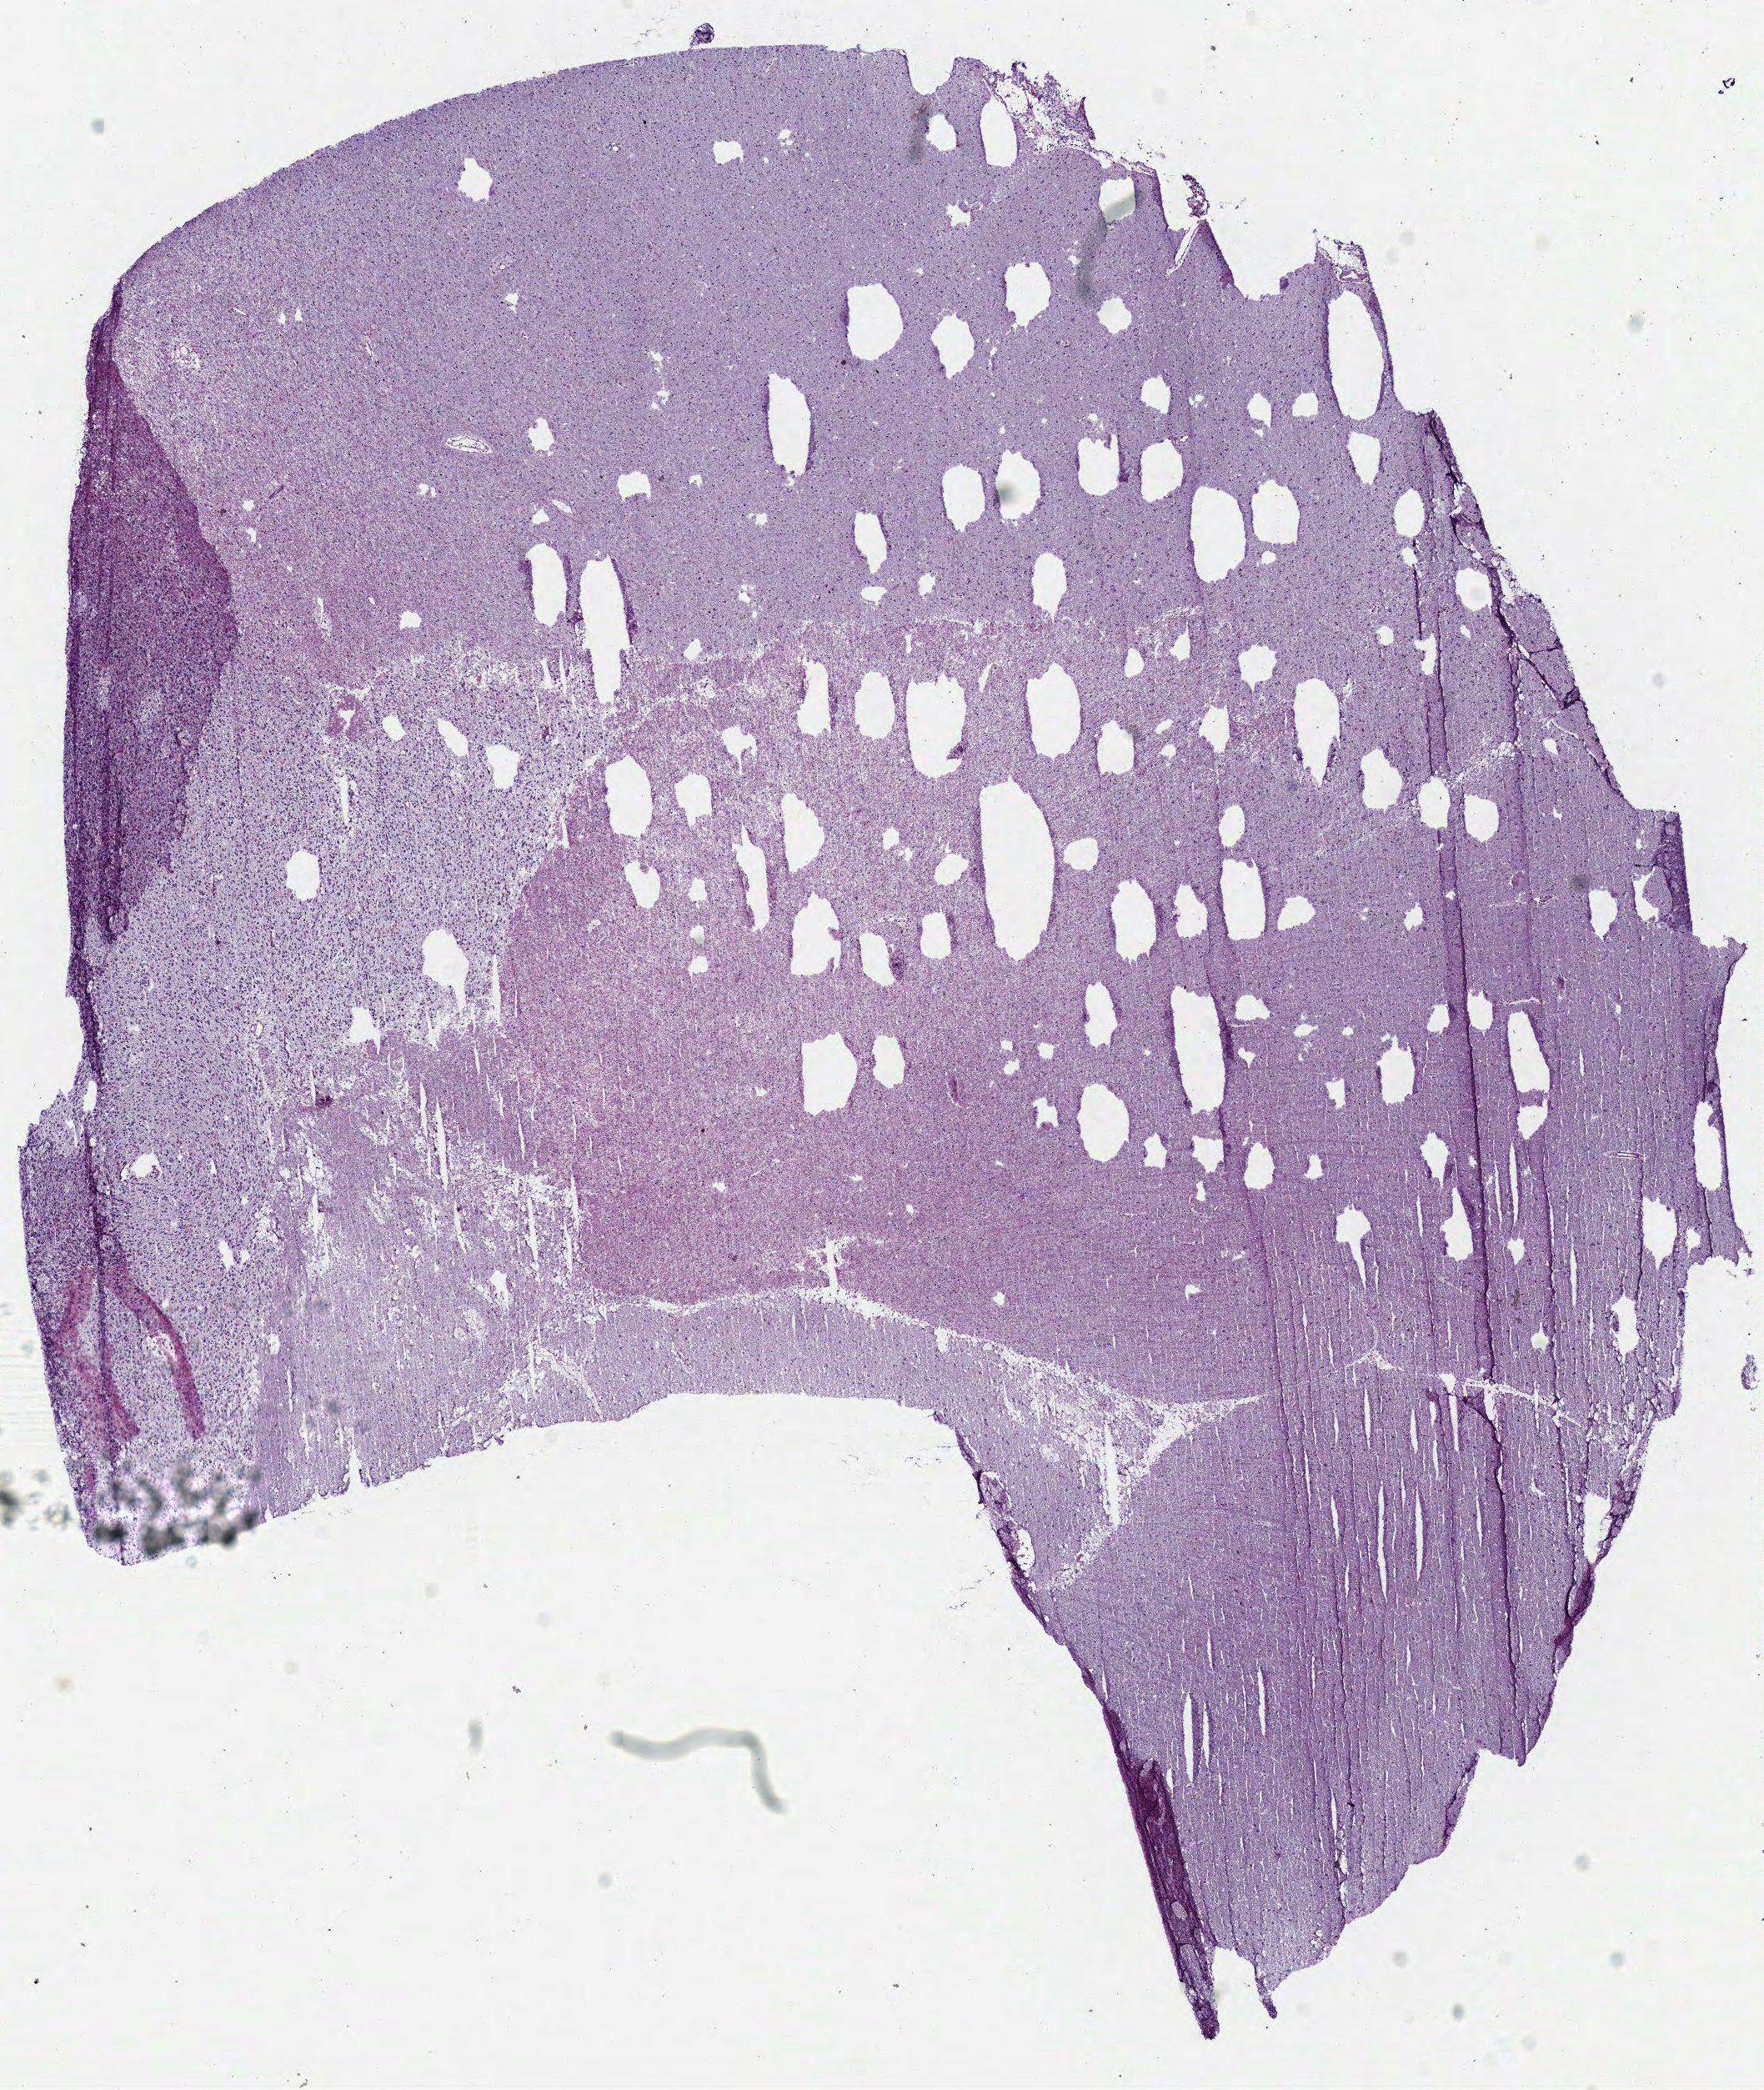
Whole-slide histology image, Hematoxylin and eosin (H&E) stained, shown as a low-resolution overview of the whole scanned area (about 8.3 x 9.9 mm, slide scanned at 40x); frozen section from the bottom of the tissue portion; brain, primary tumour sample. Male patient; age at initial diagnosis 76 years. Slide review estimates, as recorded: tumour cells 100%, tumour nuclei 60%, normal cells 0%, stromal cells 0%, necrosis 0%.
- histologic diagnosis: Glioblastoma